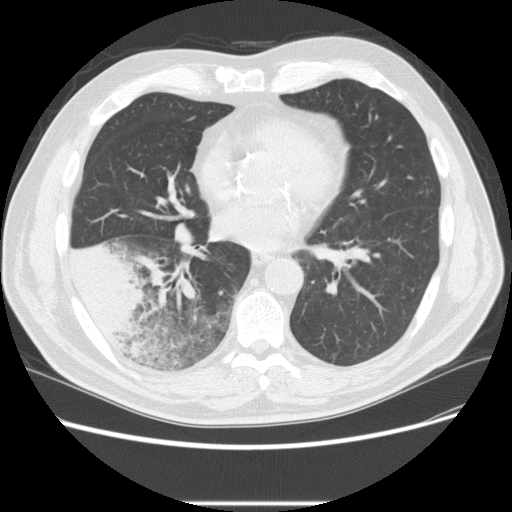
Low-dose screening chest CT, one axial slice; slice 101 of 233 in the series (ordered by position); lung window (W 1500 / L -600 HU); 2.5 mm slice thickness; 512 × 512 image matrix, field of view 380 × 380 mm.
Structures marked on this image (manually delineated by an expert):
- lesion 3 (tumor, lower lobe of right lung): bounding box (x1, y1, x2, y2) in pixels: (66, 240, 144, 343)